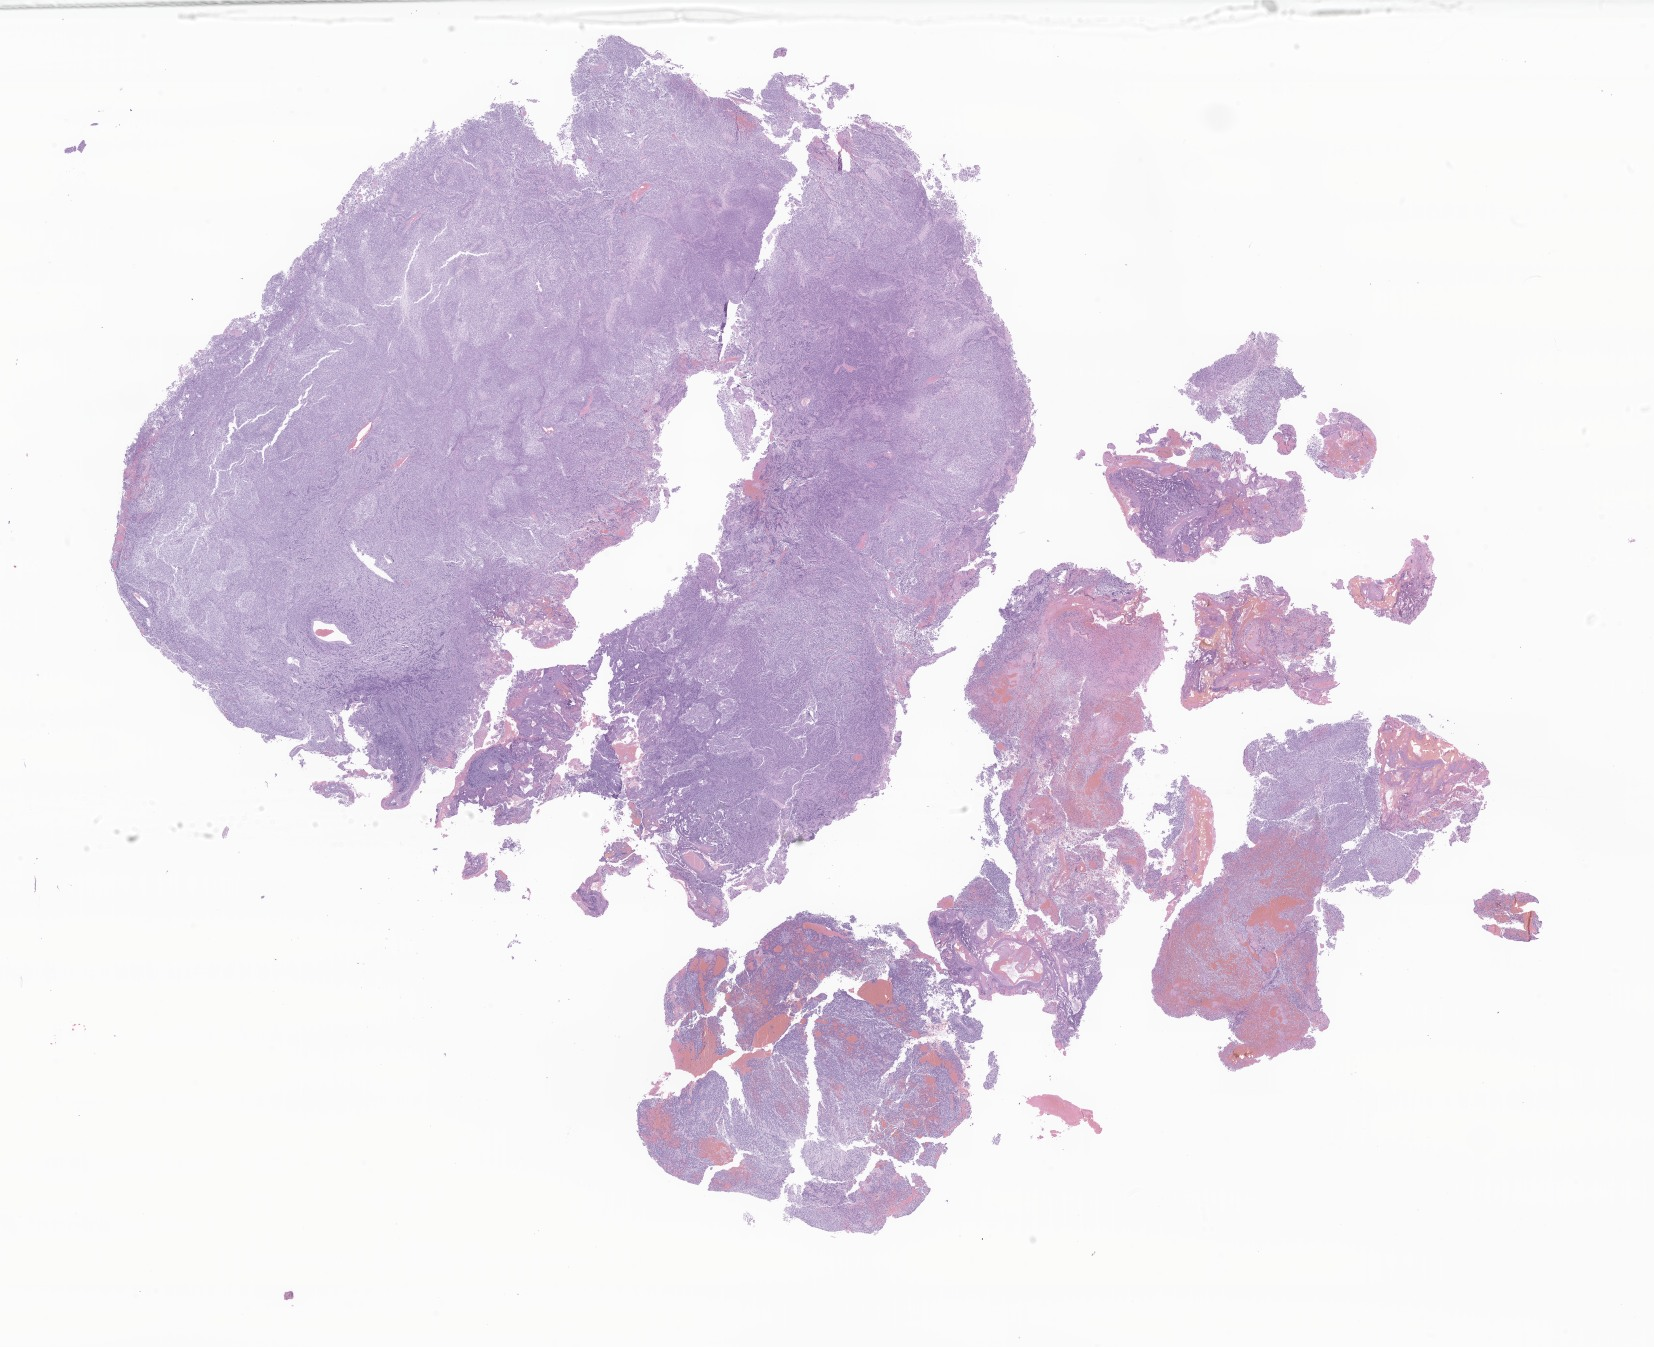
Whole-slide image, hematoxylin and eosin (H&E) stain of tumor tissue from the brain — whole scanned area (about 27.9 x 22.7 mm) shown as a low-resolution overview, formalin-fixed, paraffin-embedded (FFPE) tissue. Female patient, age 119 months (9 years 11 months).
- diagnosis: Neoplasm, malignant